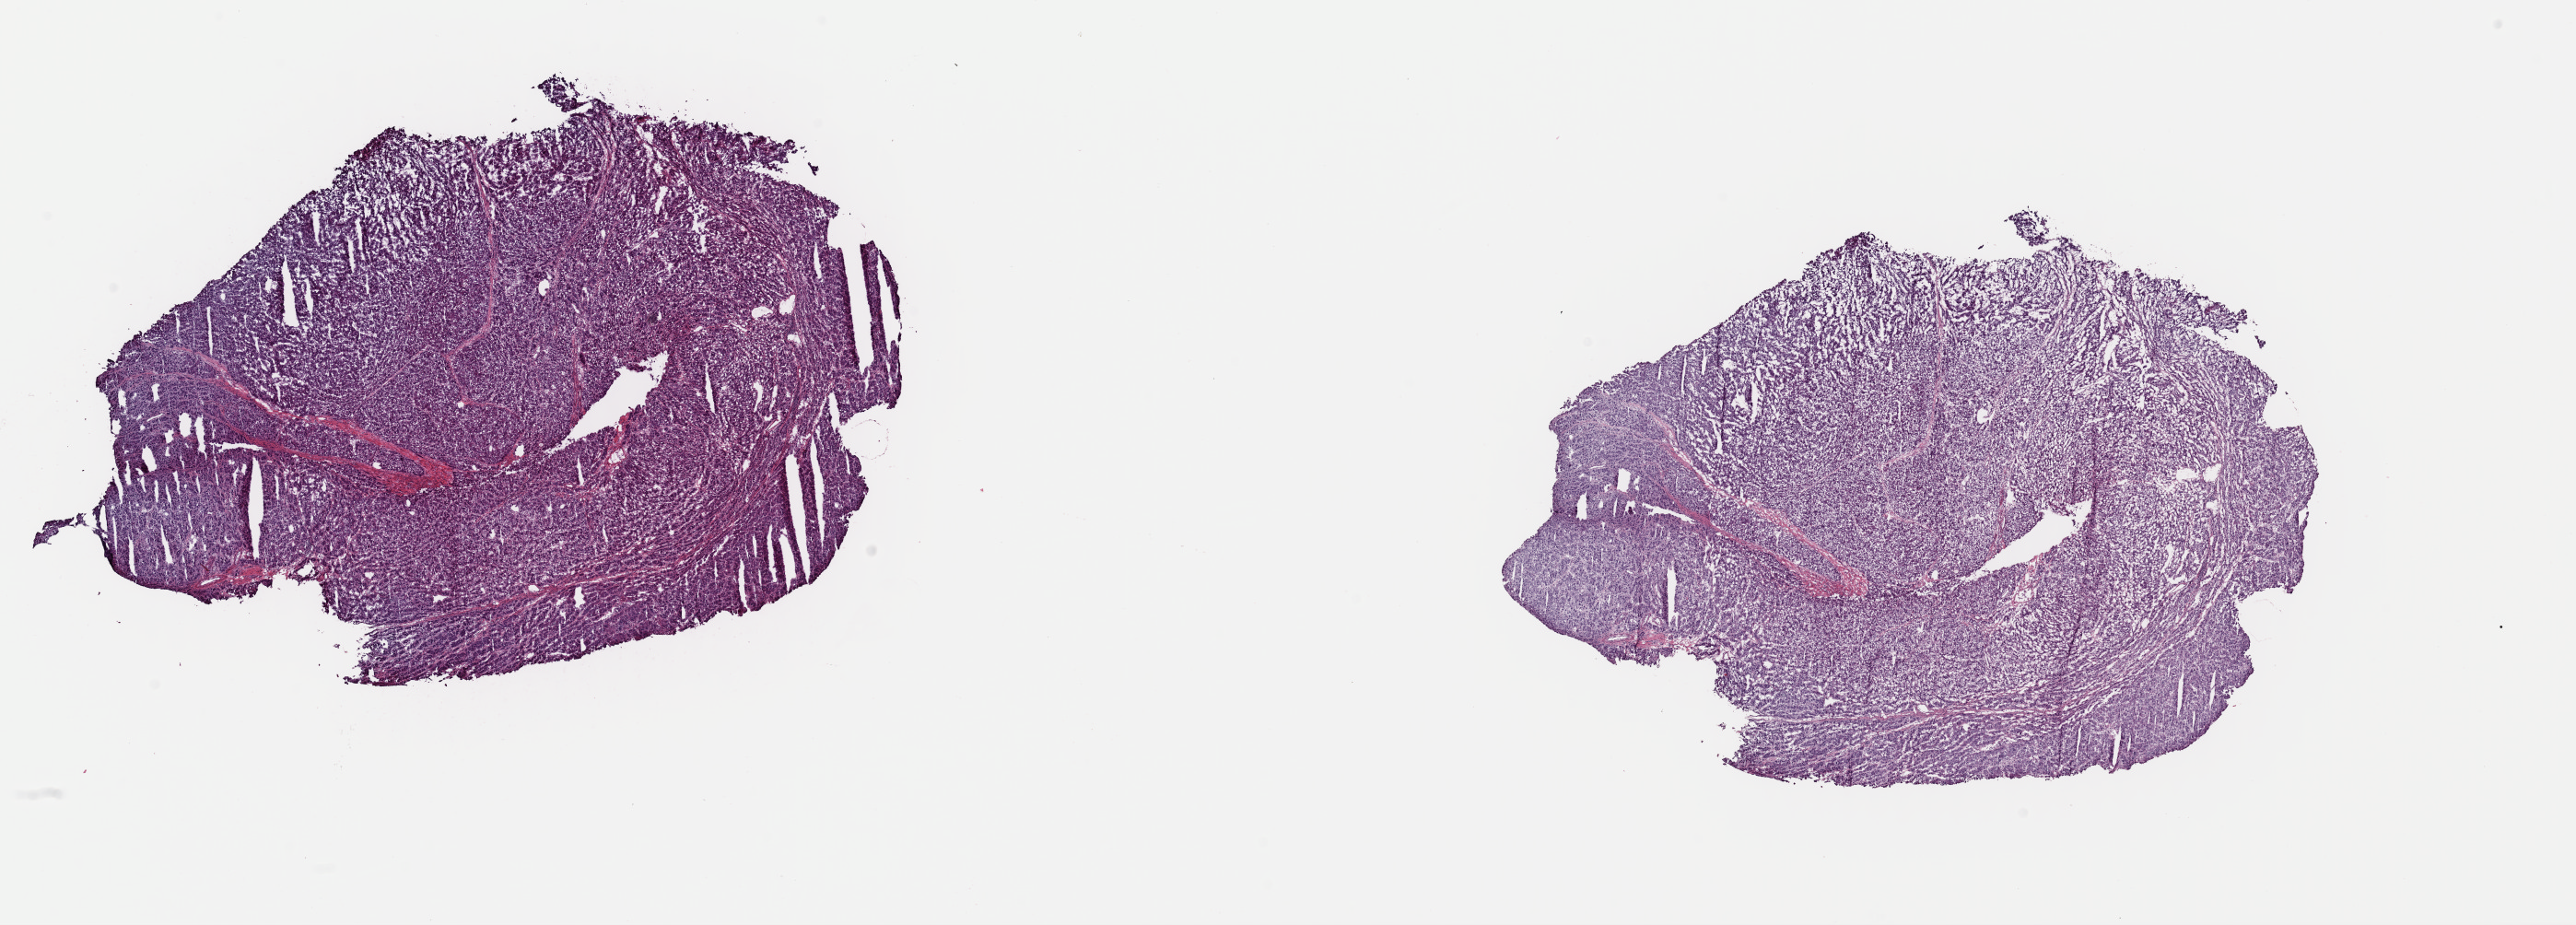
Whole-slide histology image, H&E — a low-resolution overview of the entire scanned area, about 22.1 x 7.9 mm, frozen section from the top of the tissue portion, liver, primary tumour sample. Male, age 53 years at initial diagnosis. Histologic grade: G2 (moderately differentiated). Slide review estimates, as recorded: tumour cells 100%, tumour nuclei 96%, normal cells 0%, stromal cells 0%, necrosis 0%. Inflammatory infiltration, as recorded: lymphocyte infiltration 0%, monocyte infiltration 0%, neutrophil infiltration 0%.
AJCC pathologic stage: IIIA. TNM: T3a N0 M0. Pathologic diagnosis: Hepatocellular carcinoma, NOS.